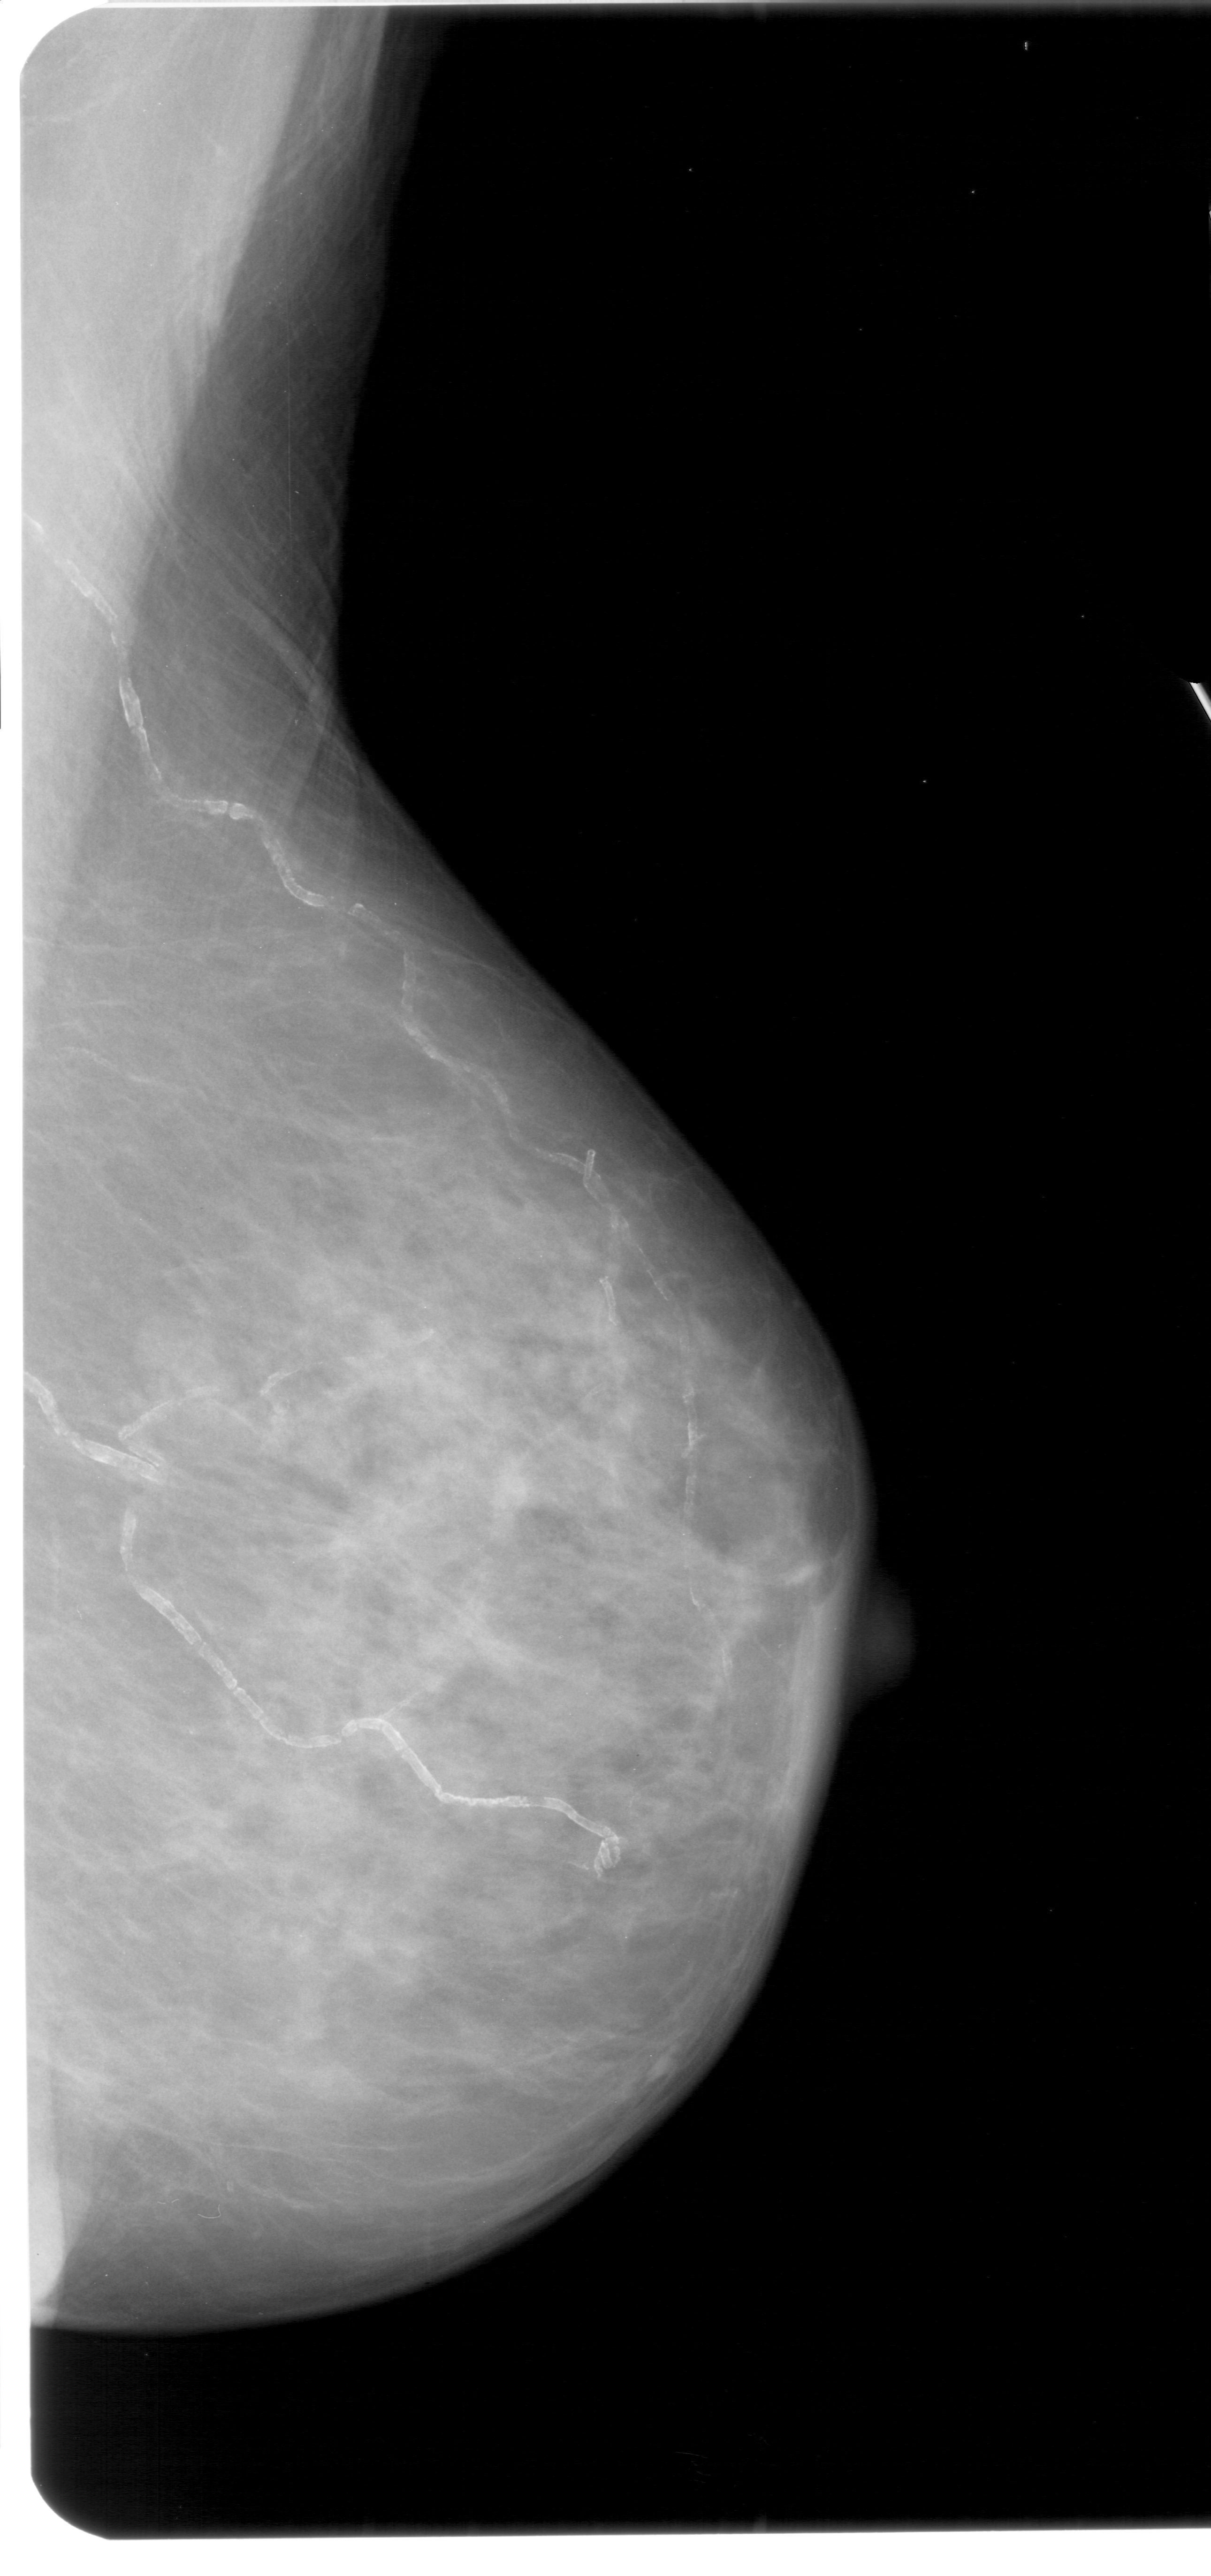
Scanned film-screen mammogram; right breast; MLO view; BI-RADS breast density category 3 (scale 1–4).
Finding: mass, shape architectural distortion, margins spiculated; BI-RADS assessment category 5; pathology (as recorded): malignant.